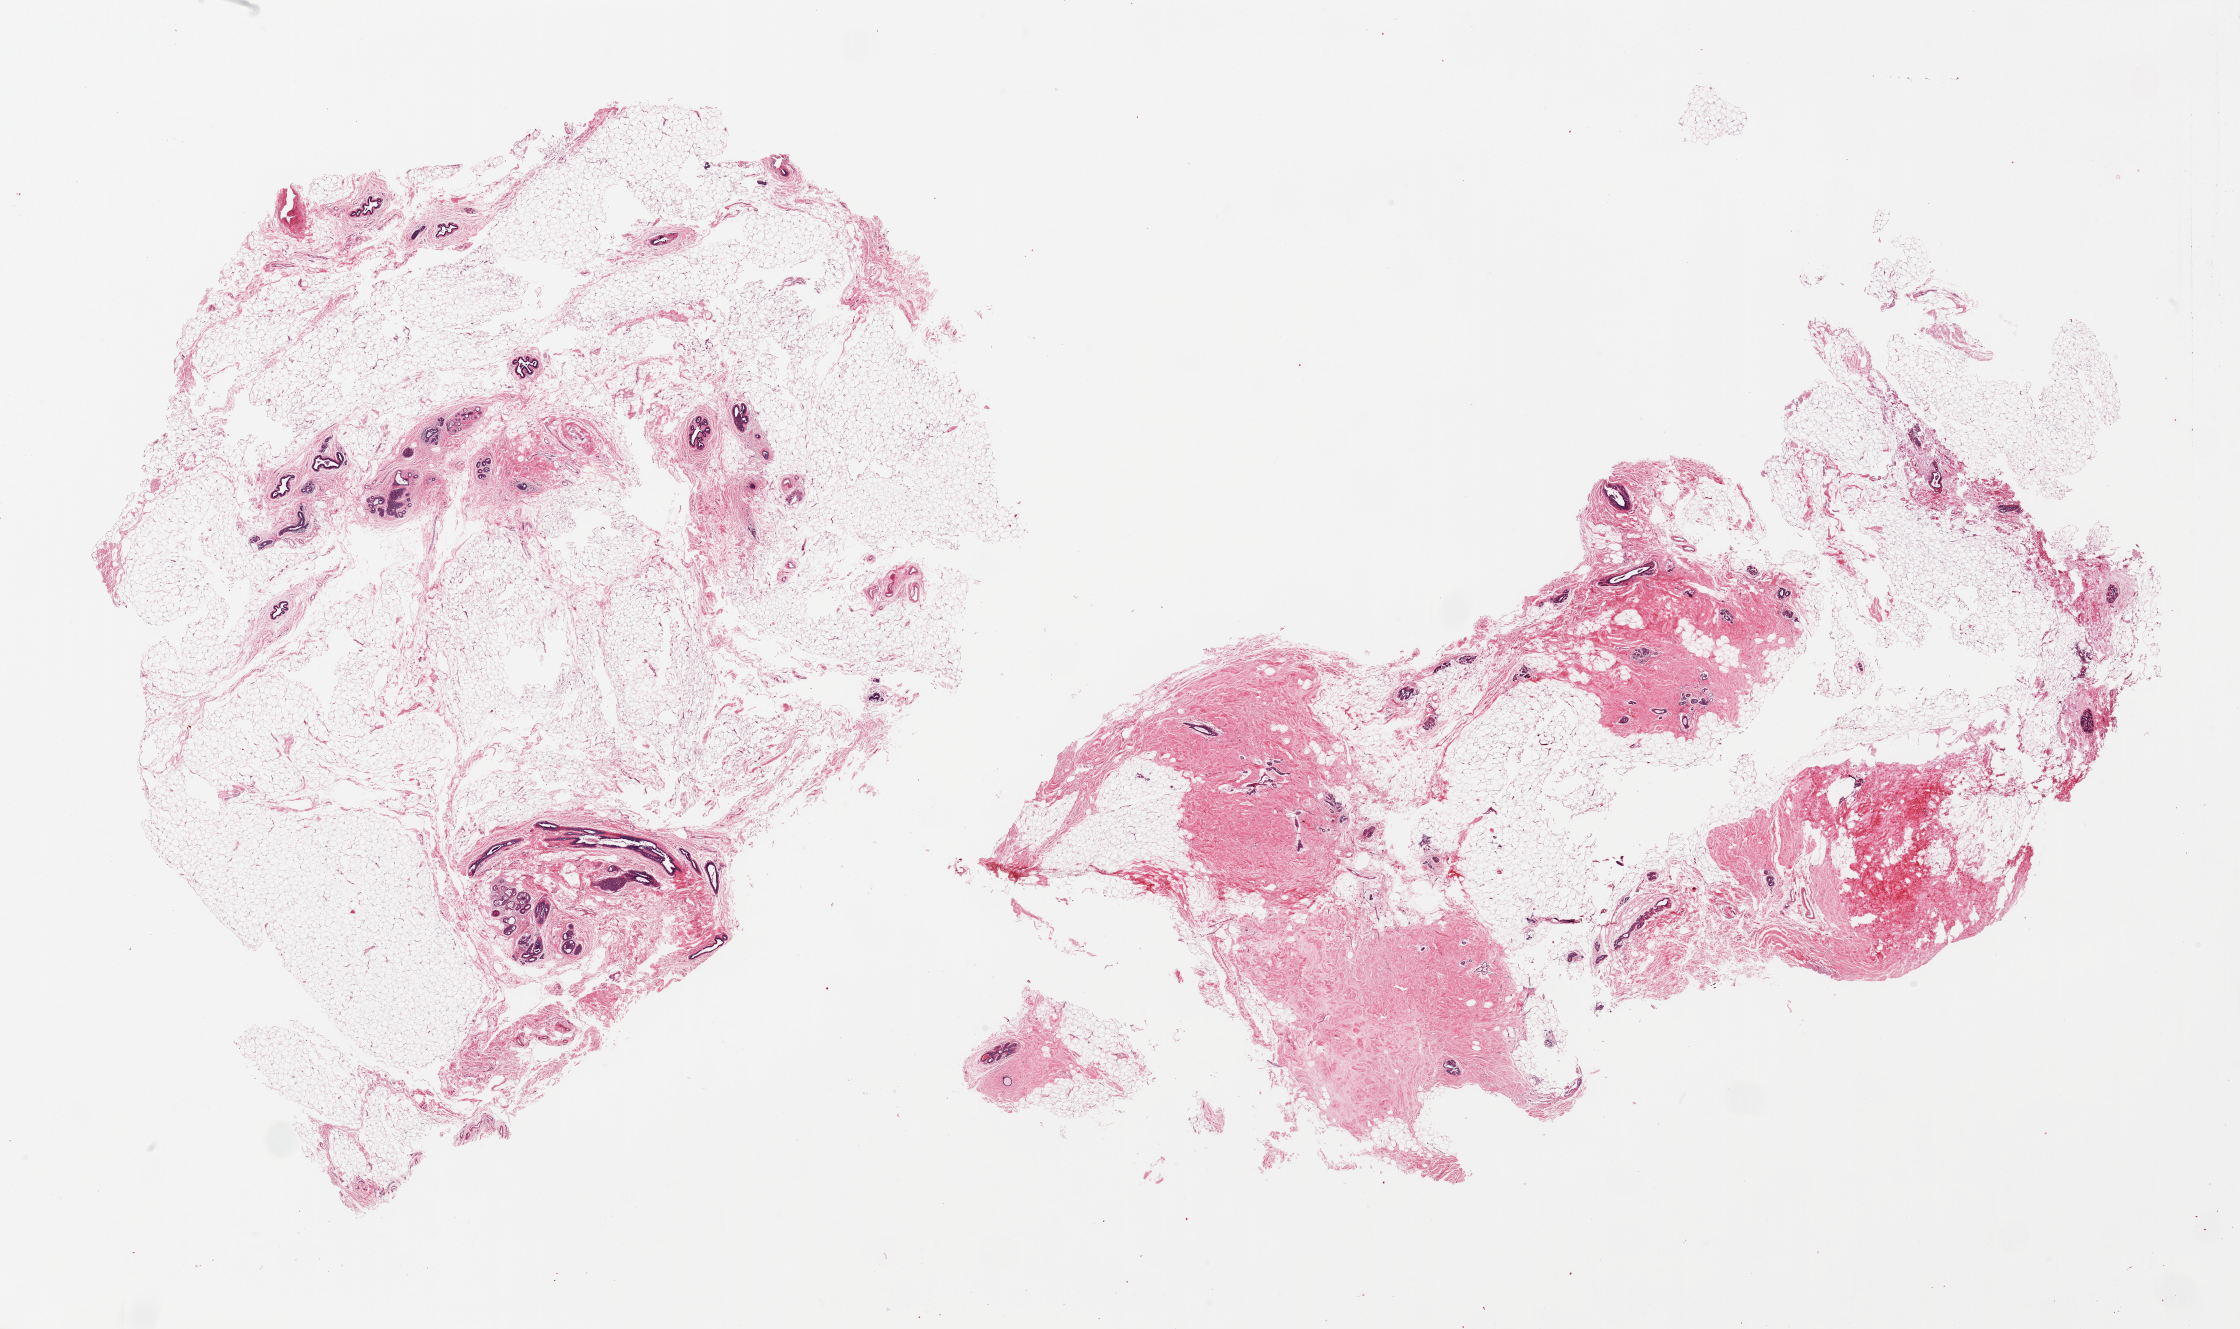
Whole-slide image, haematoxylin and eosin stain — whole scanned area (about 35.4 x 21.0 mm) shown as a low-resolution overview; PAXgene-fixed paraffin-embedded (PFPE) section; section of breast (target tissue); donor tissue sample.
• reviewer comment on this tissue sample: 2 pieces, ductal/lobular elements well preserved; foci of duct epithelial hyerplasia